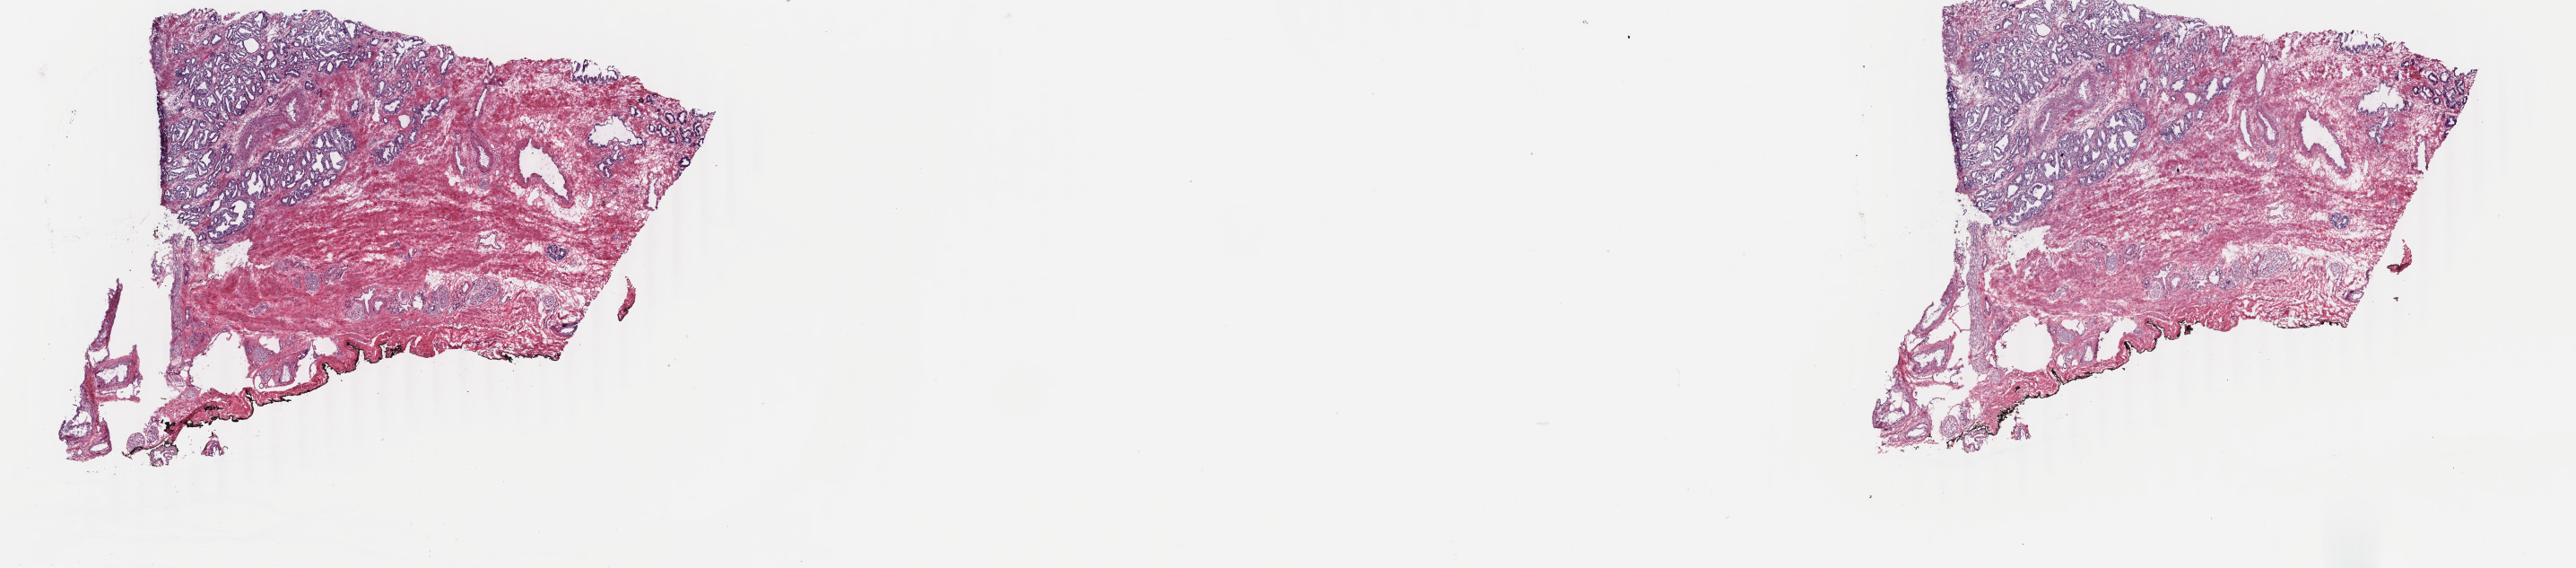
H&E-stained whole-slide image, a low-resolution overview of the entire scanned area, about 22.8 x 5.0 mm (acquisition: 40x scan), frozen section from the top of the tissue portion, prostate, primary tumour sample. Male patient; age at initial diagnosis 59 years. Gleason score: 7 (3+4). Composition of this section per pathologist review: tumour cells 40%, tumour nuclei 60%, normal cells 3%, stromal cells 57%, necrosis 0%. Infiltration values recorded for this section: lymphocyte infiltration 0%, monocyte infiltration 0%, neutrophil infiltration 0%.
* laterality: bilateral
* histologic diagnosis: Adenocarcinoma, NOS (prostate gland)
* lymph nodes positive (case pathology): 0 of 2 examined